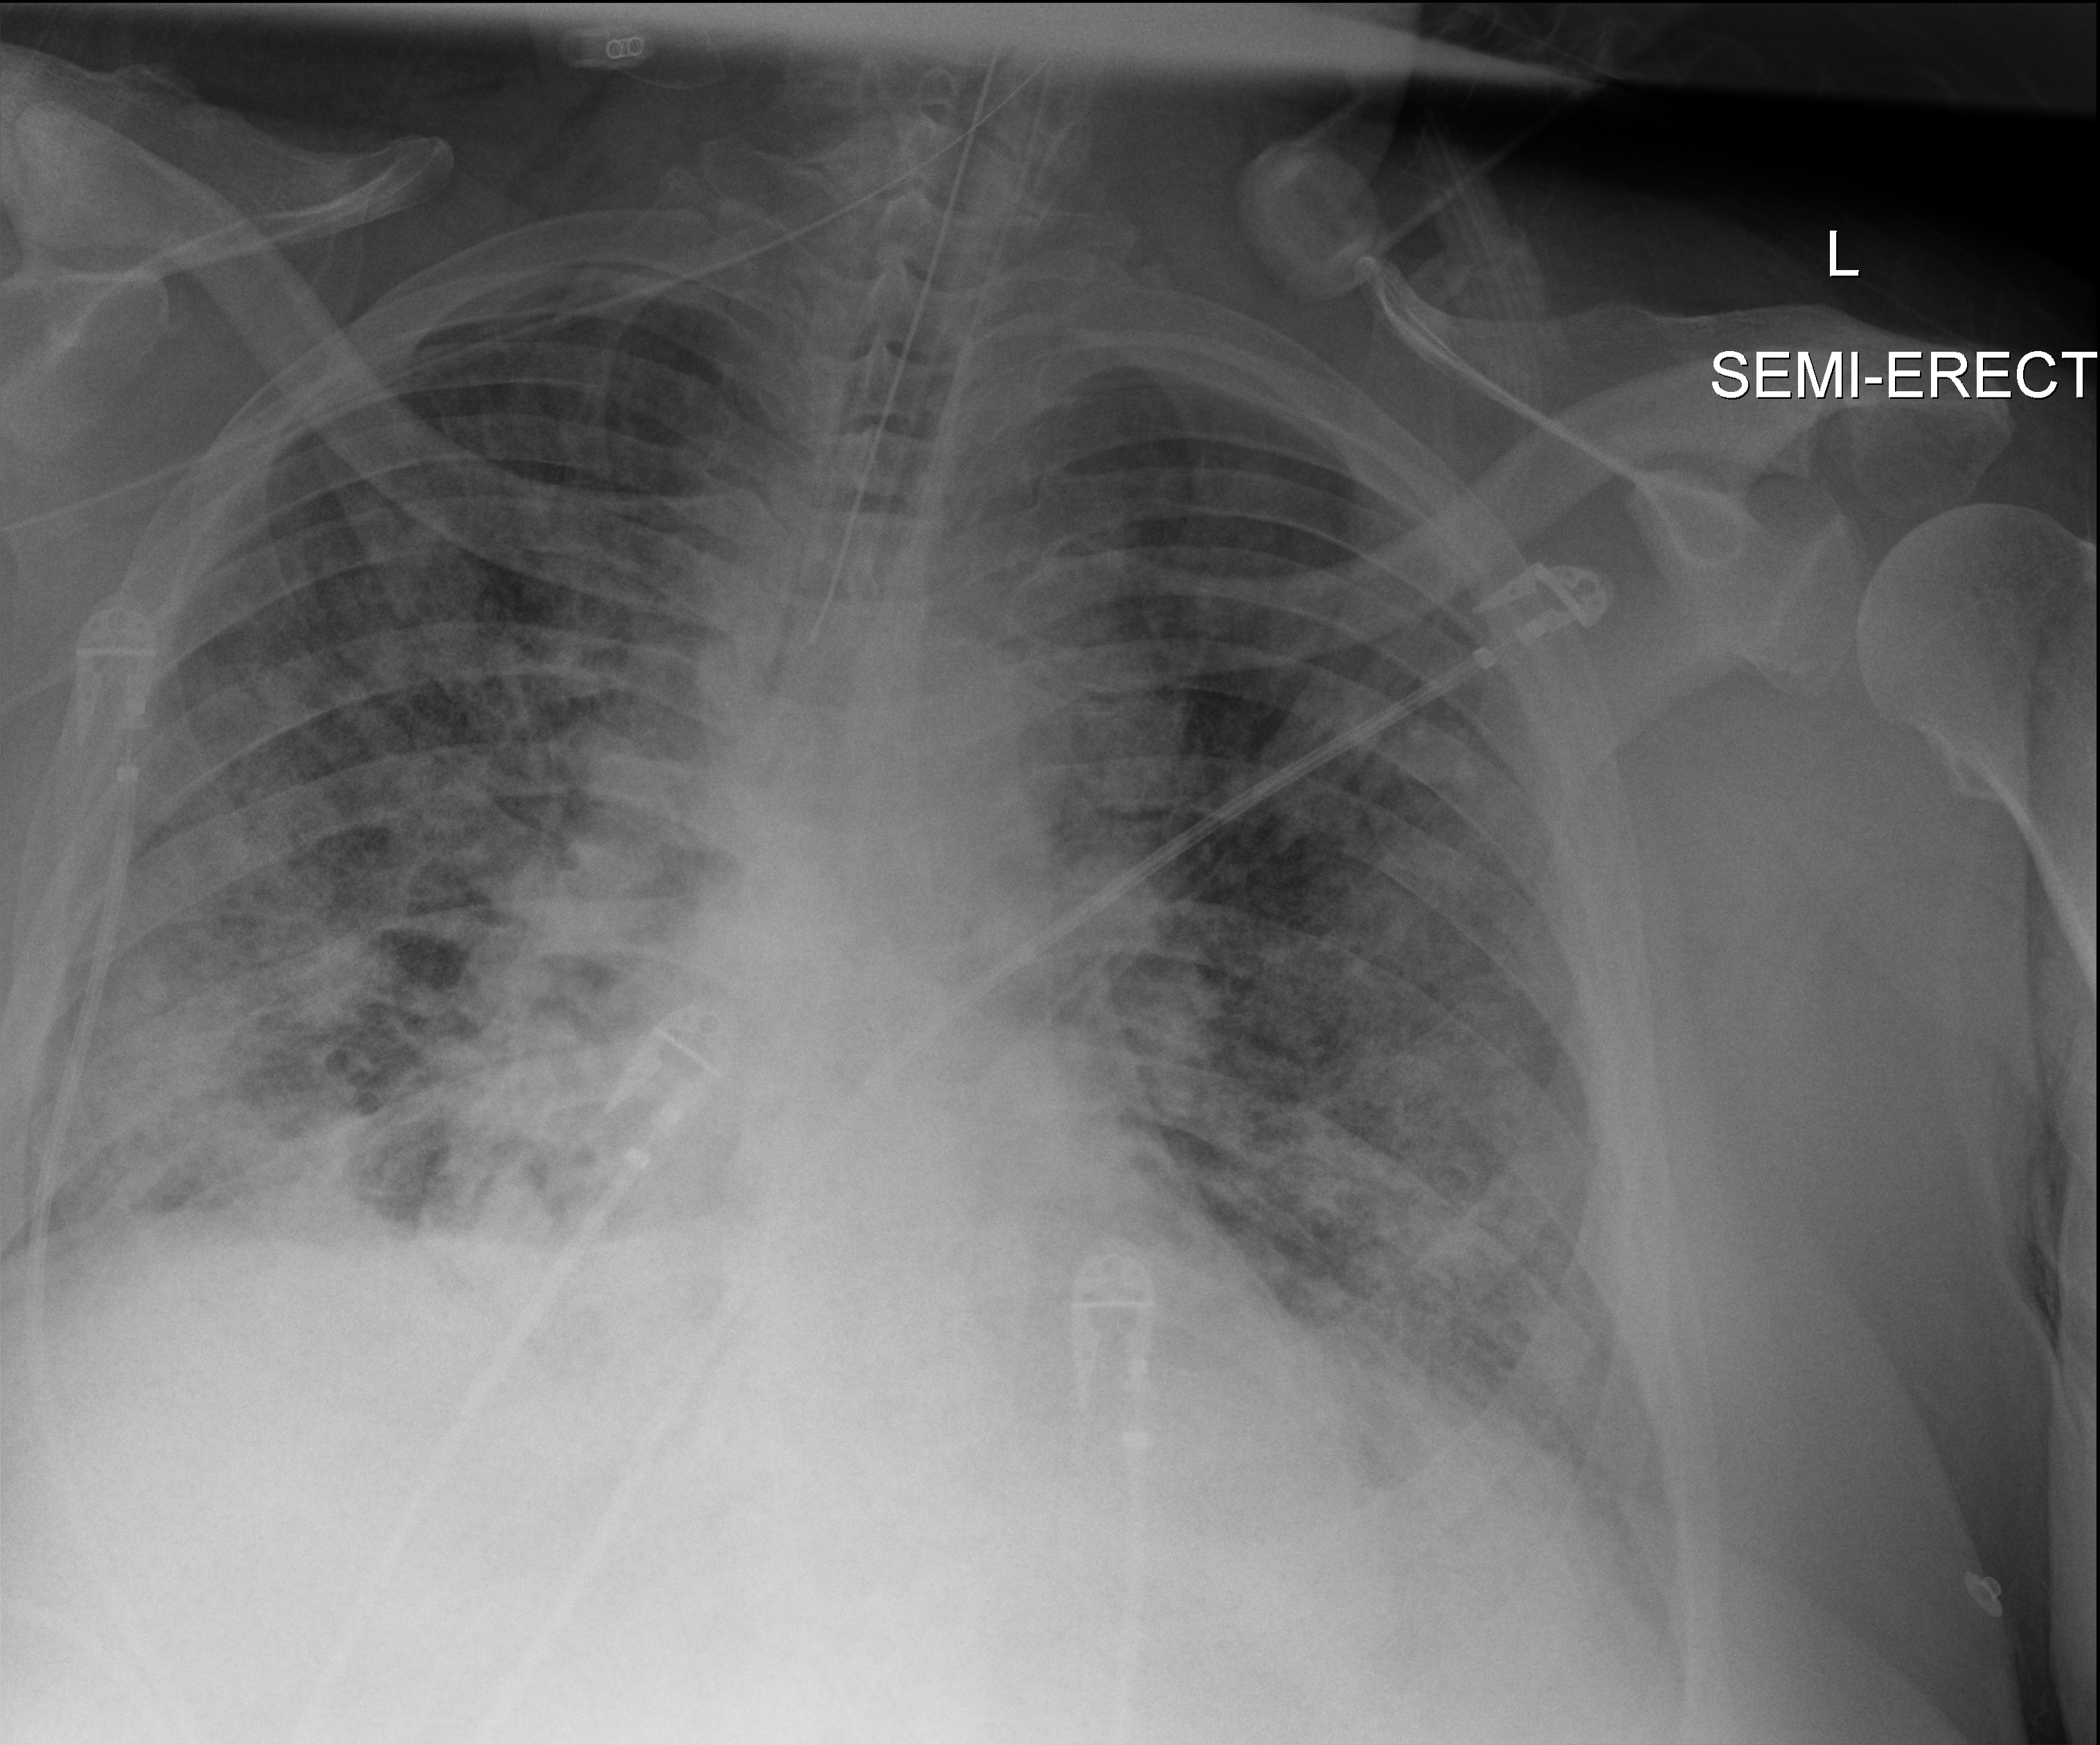
Portable chest radiograph, anteroposterior (AP) projection. Male patient hospitalised with COVID-19, age 60–74 years.
Hospital-stay facts (about this admission, not read from this image; timing relative to this image not recorded): length of hospital stay: 34 days; chronic kidney disease (admission record): no.